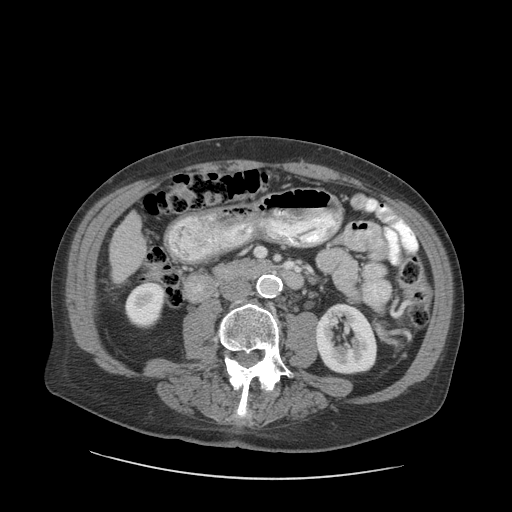
Contrast-enhanced abdominal CT (liver protocol), one axial slice; slice 23 of 89 in the series (ordered by position); reconstruction kernel STANDARD; soft-tissue window (W 400 / L 40 HU); 512 × 512 image matrix, field of view 420 × 420 mm. From the clinical record (not read from this slice): diagnosis: hepatocellular carcinoma (patient treated with transarterial chemoembolisation; whether this scan precedes or follows treatment is not stated here); TNM stage (as recorded): Stage-I; Child-Pugh class: A; tumour nodularity: uninodular.
Annotated regions visible in this slice (semi-automatically segmented with operator editing):
- liver parenchyma outside the tumour (the mass and vessels are separate outlines, so this box may not span the whole liver): bounding box [x1, y1, x2, y2] px = [110, 212, 146, 282]